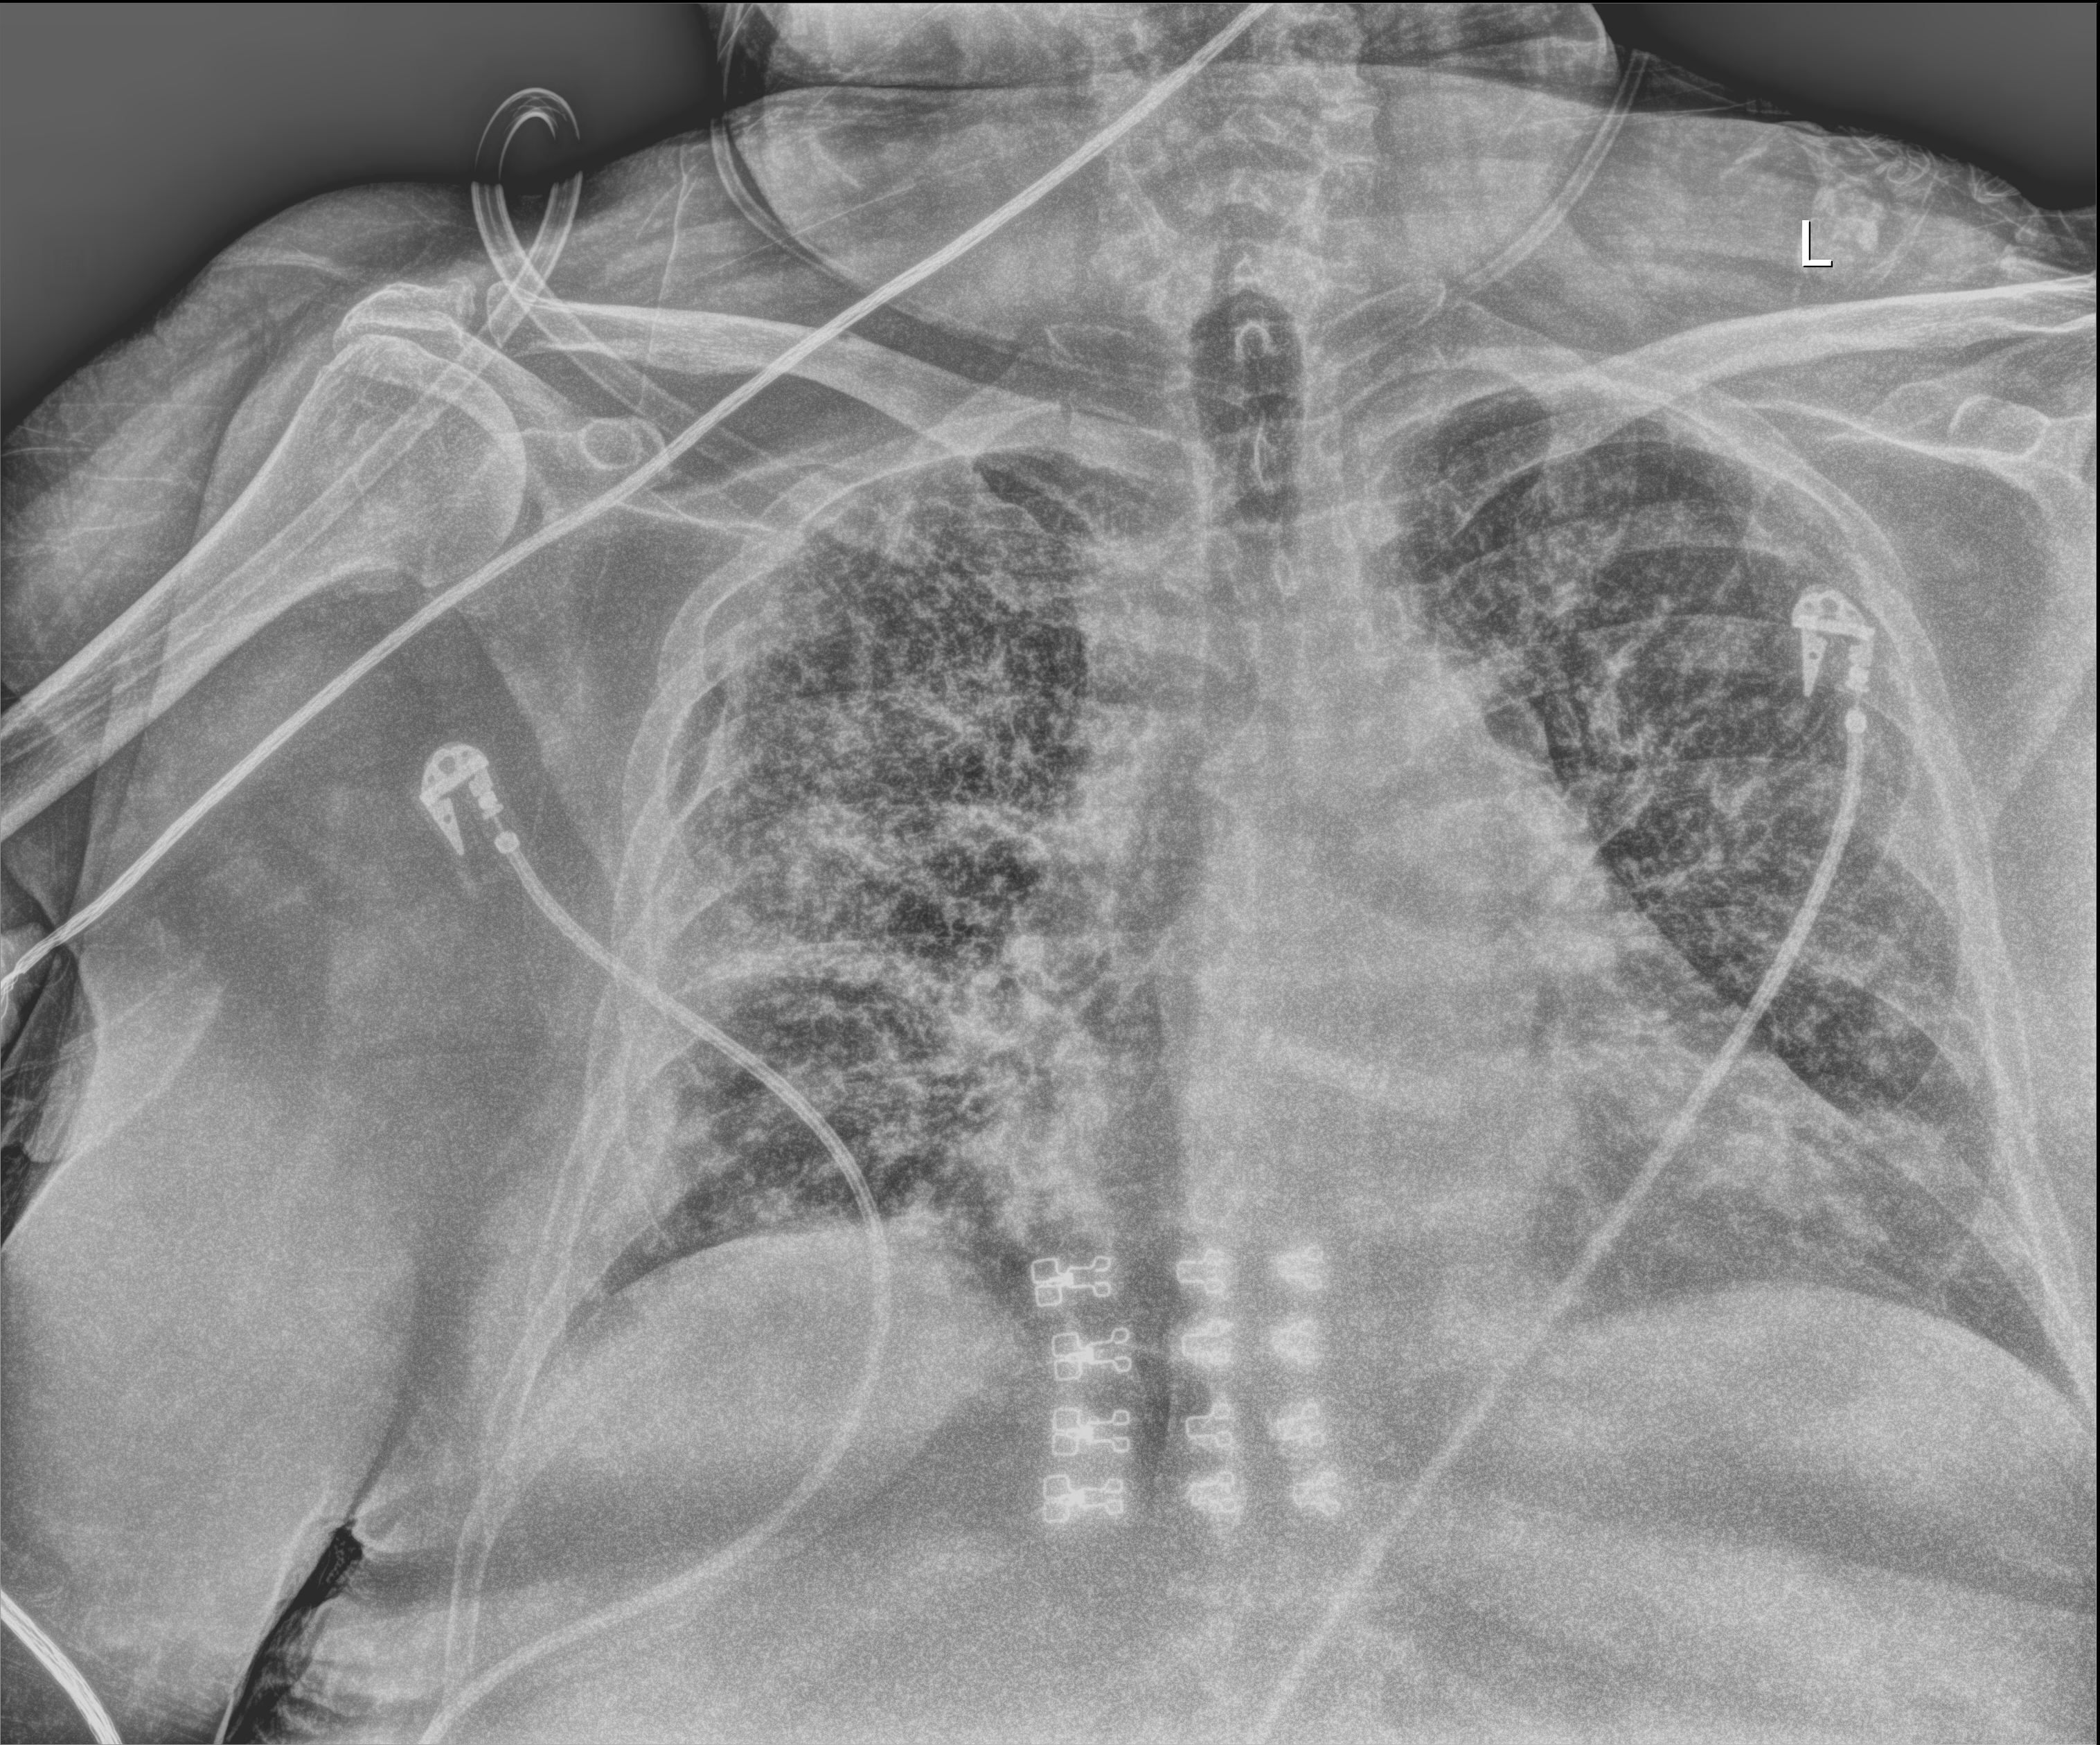
Bedside chest radiograph (digital radiography); anteroposterior (AP) projection. Female patient hospitalised with COVID-19, age 60–74 years.
Hospital-stay facts (about this admission, not read from this image; timing relative to this image not recorded):
- admitted to intensive care during this hospital stay: yes
- chronic kidney disease (admission record): no